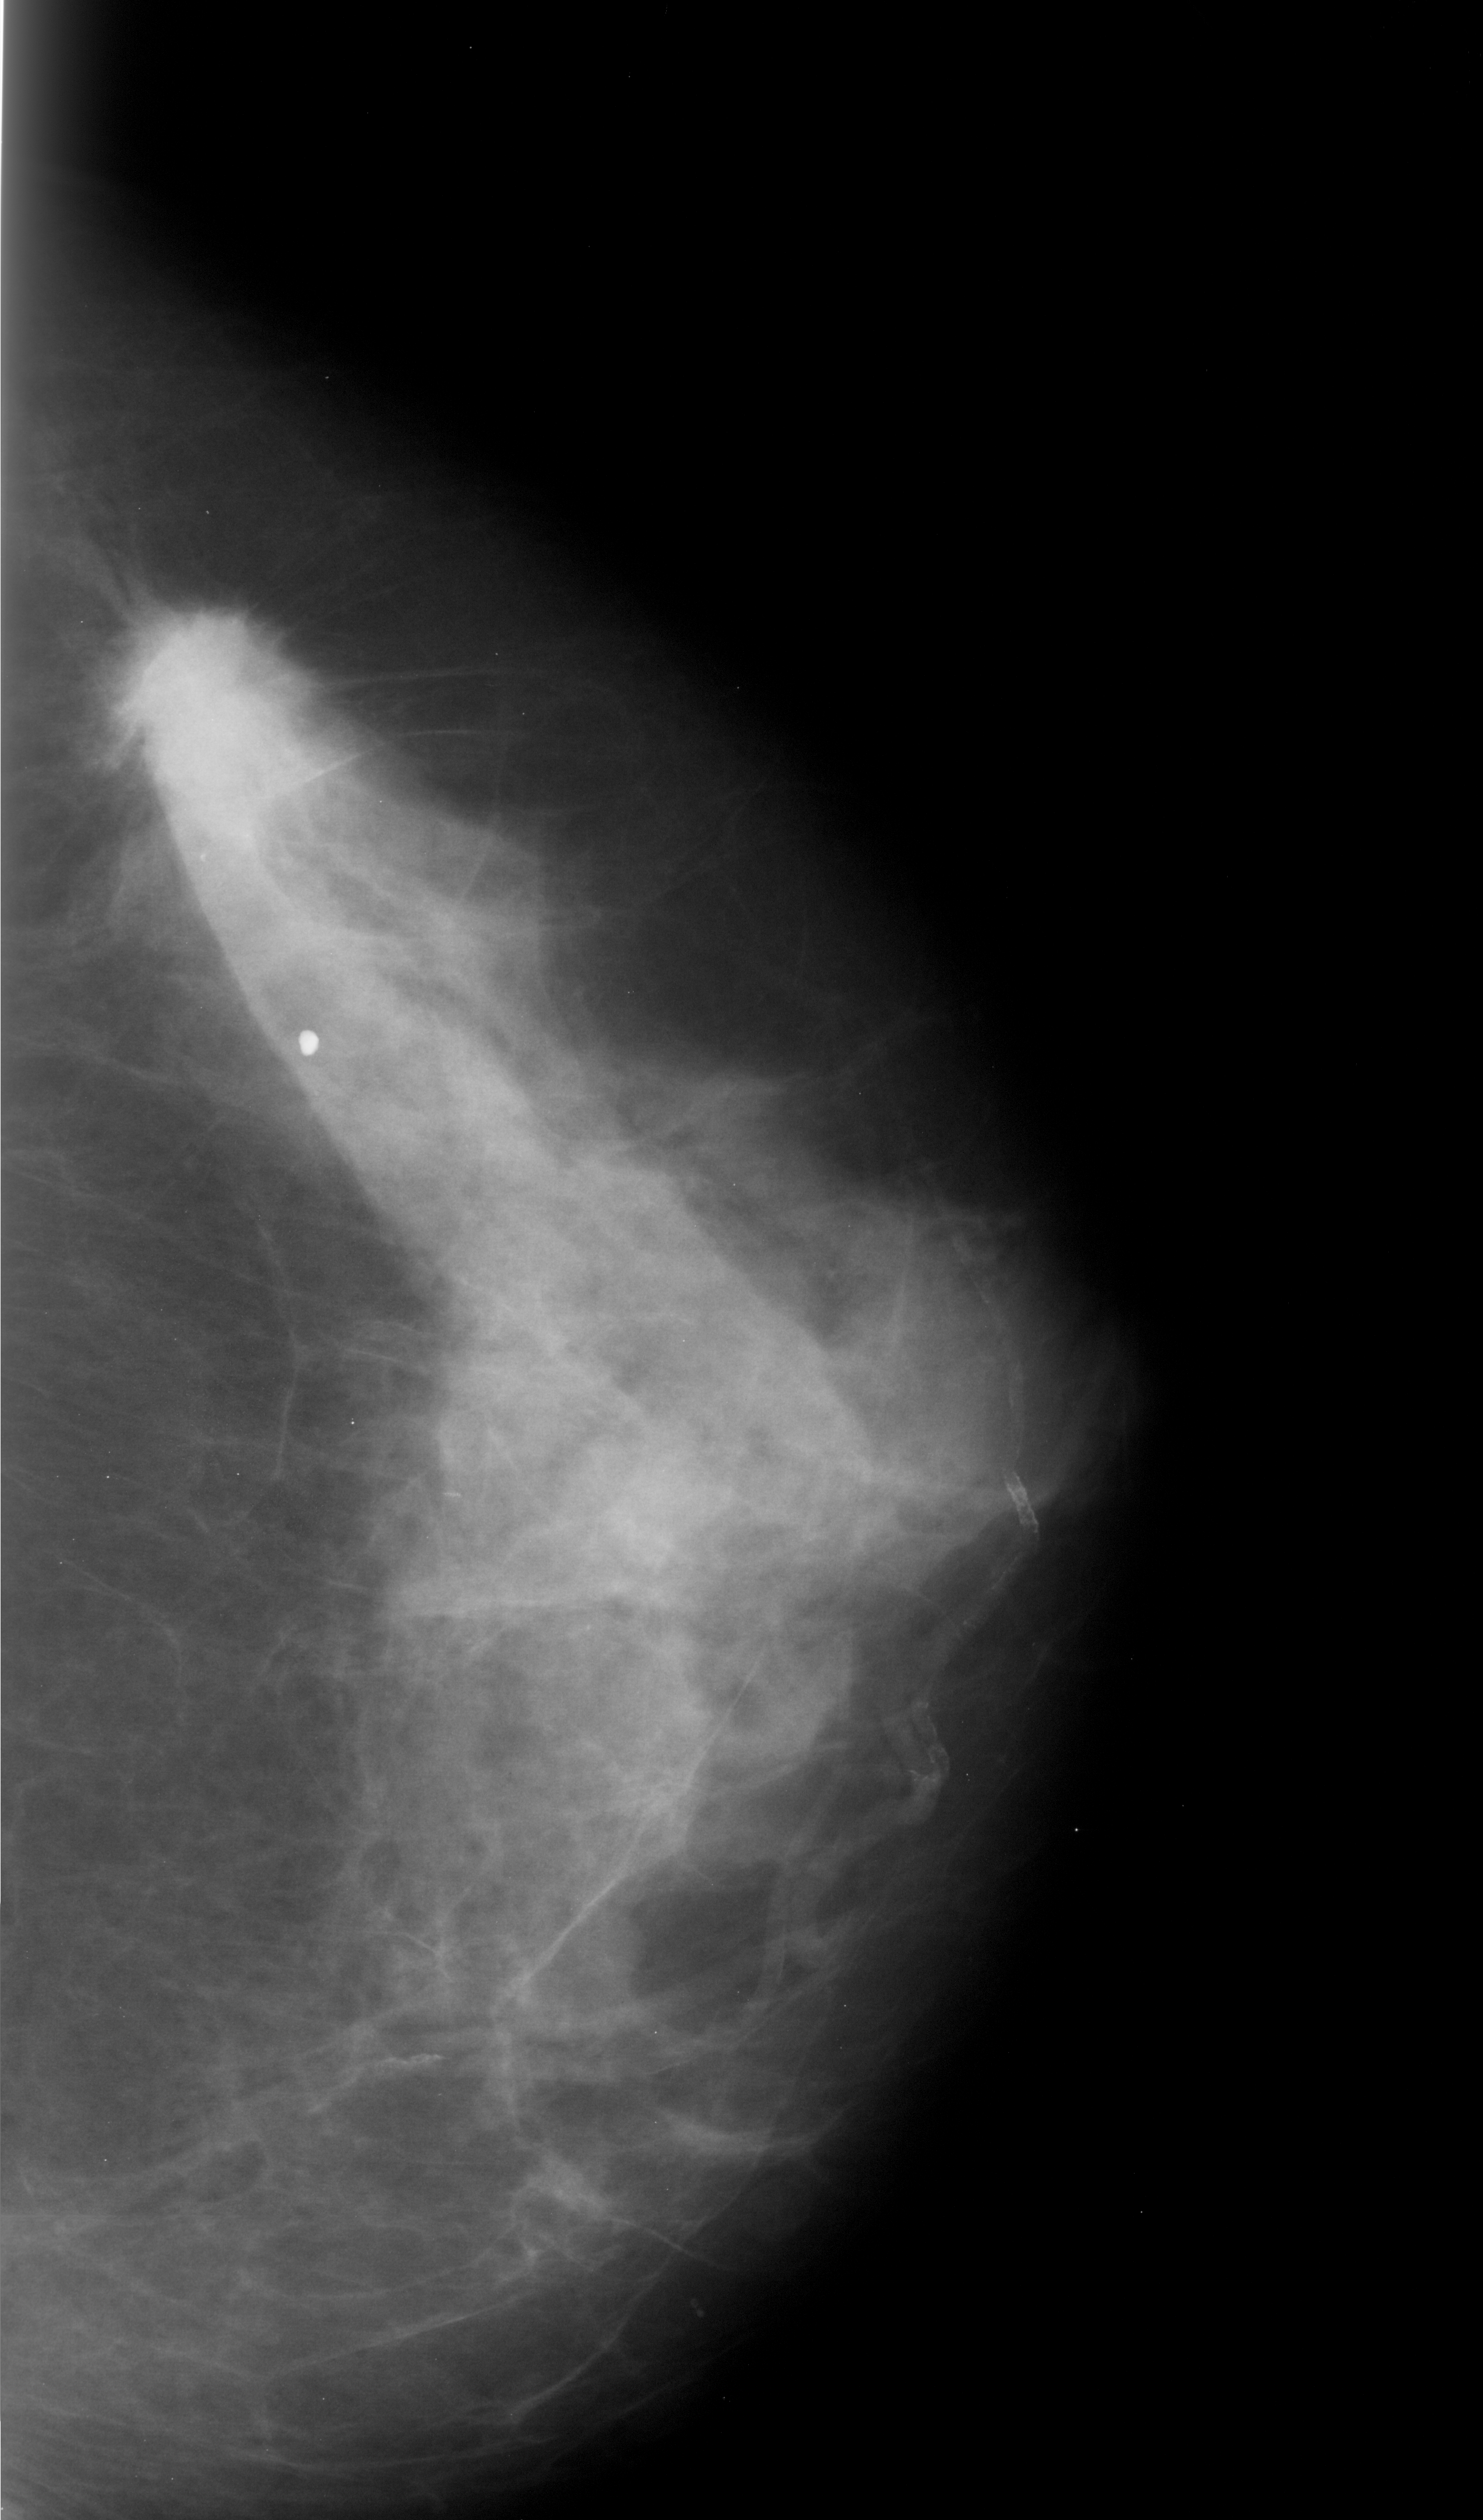
Scanned film-screen mammogram. Right breast. CC view. BI-RADS breast density category 3 (scale 1–4). 1483 × 2520 image matrix.
Expert-marked regions of interest on this image (one box per marked abnormality):
- mass, shape irregular, margins spiculated; BI-RADS assessment category 5; pathology result (as recorded, not read from the image): malignant: box from (x=93, y=584) to (x=299, y=768) px